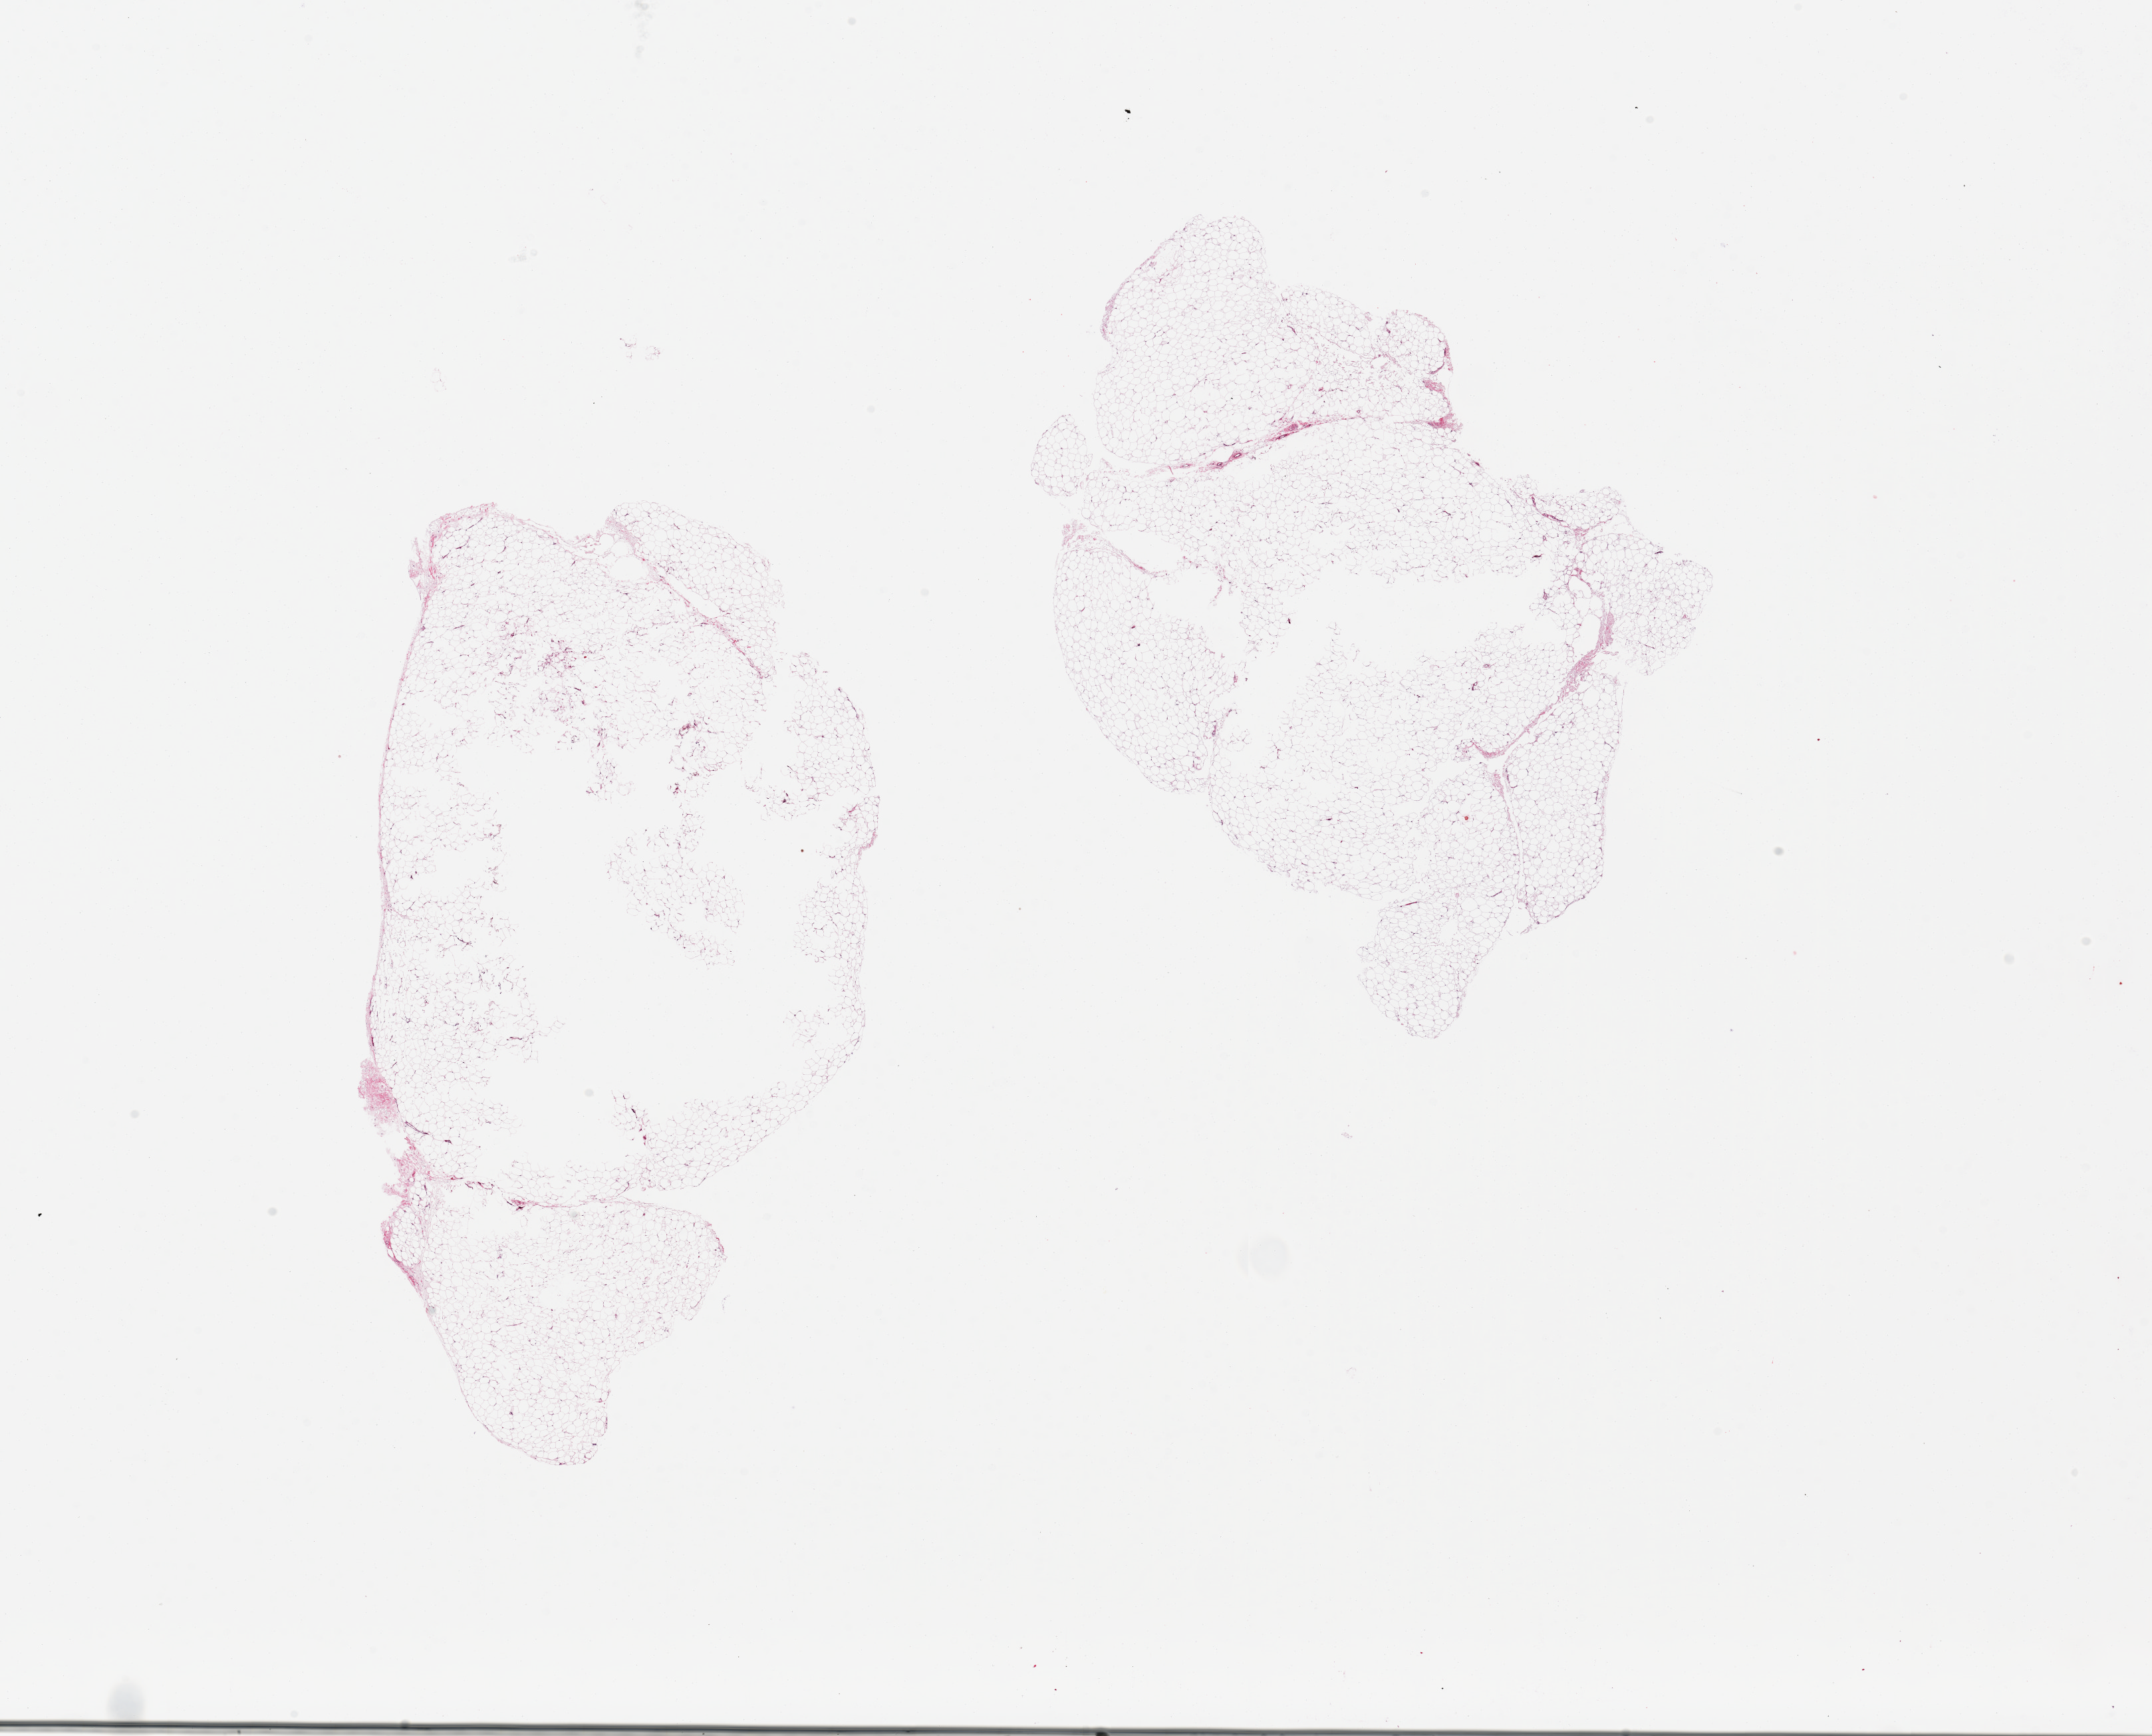
Hematoxylin and eosin (H&E) whole-slide image, low-resolution overview of the scanned area, about 25.6 x 20.6 mm (slide scanned at 20x). PAXgene-fixed paraffin-embedded (PFPE) section. Section of adipose tissue (target tissue). Tissue donor sample.
Reviewer comment on this tissue sample: 2 aliquots, ~9x6mm.